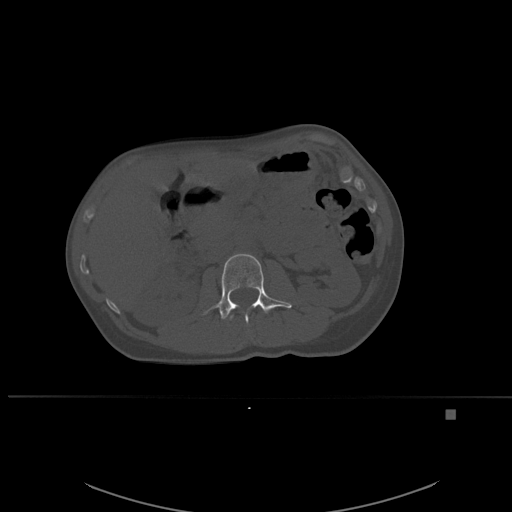
CT including the spine, one axial slice. Slice 240 of 537 in the series (ordered by position). Bone window (W 1800 / L 400 HU). 1.5 mm slice thickness. 512 × 512 image matrix, field of view 440 × 440 mm. Female patient, age 45 years. From the clinical record (not read from this slice): primary cancer: lung.
Annotated regions visible in this slice (semi-automatic segmentation, software-assisted and operator-edited):
- L1 vertebra: bounding box <228,314,234,321> (left, top, right, bottom; pixels)
- L2 vertebra: <204,253,292,323>